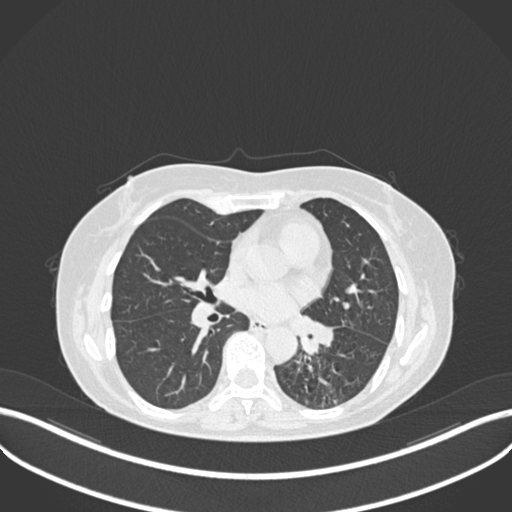
Chest CT, one axial slice; reconstruction kernel B30f; lung window (W 1500 / L -600 HU); 1 mm slice thickness; 512 × 512 image matrix. Female patient, age 63 years. Case-level facts recorded for this patient, not image findings: clinical TNM (as recorded): T1b N0 M0; histopathological grade: G2-3.
Outlined on this slice (rectangle marked by the reading radiologist):
- lung tumour (recorded histology: adenocarcinoma): bounding box [x1, y1, x2, y2] px = [288, 308, 347, 360]